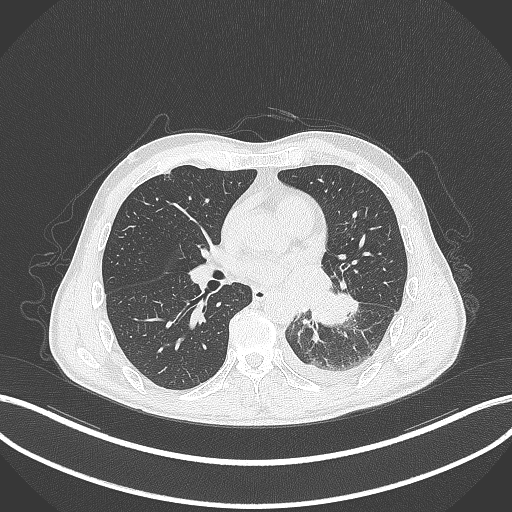
Chest CT, one axial slice. Reconstruction kernel B70f. Lung window (W 1500 / L -600 HU). 512 × 512 image matrix, field of view 400 × 400 mm. Male patient, age 47 years. Case-level facts recorded for this patient, not image findings: clinical TNM (as recorded): T3 N1 M1c.
Structures marked on this image (bounding box drawn by a radiologist):
- lung tumour (recorded histology: small cell carcinoma): box from (x=307, y=289) to (x=353, y=328) px